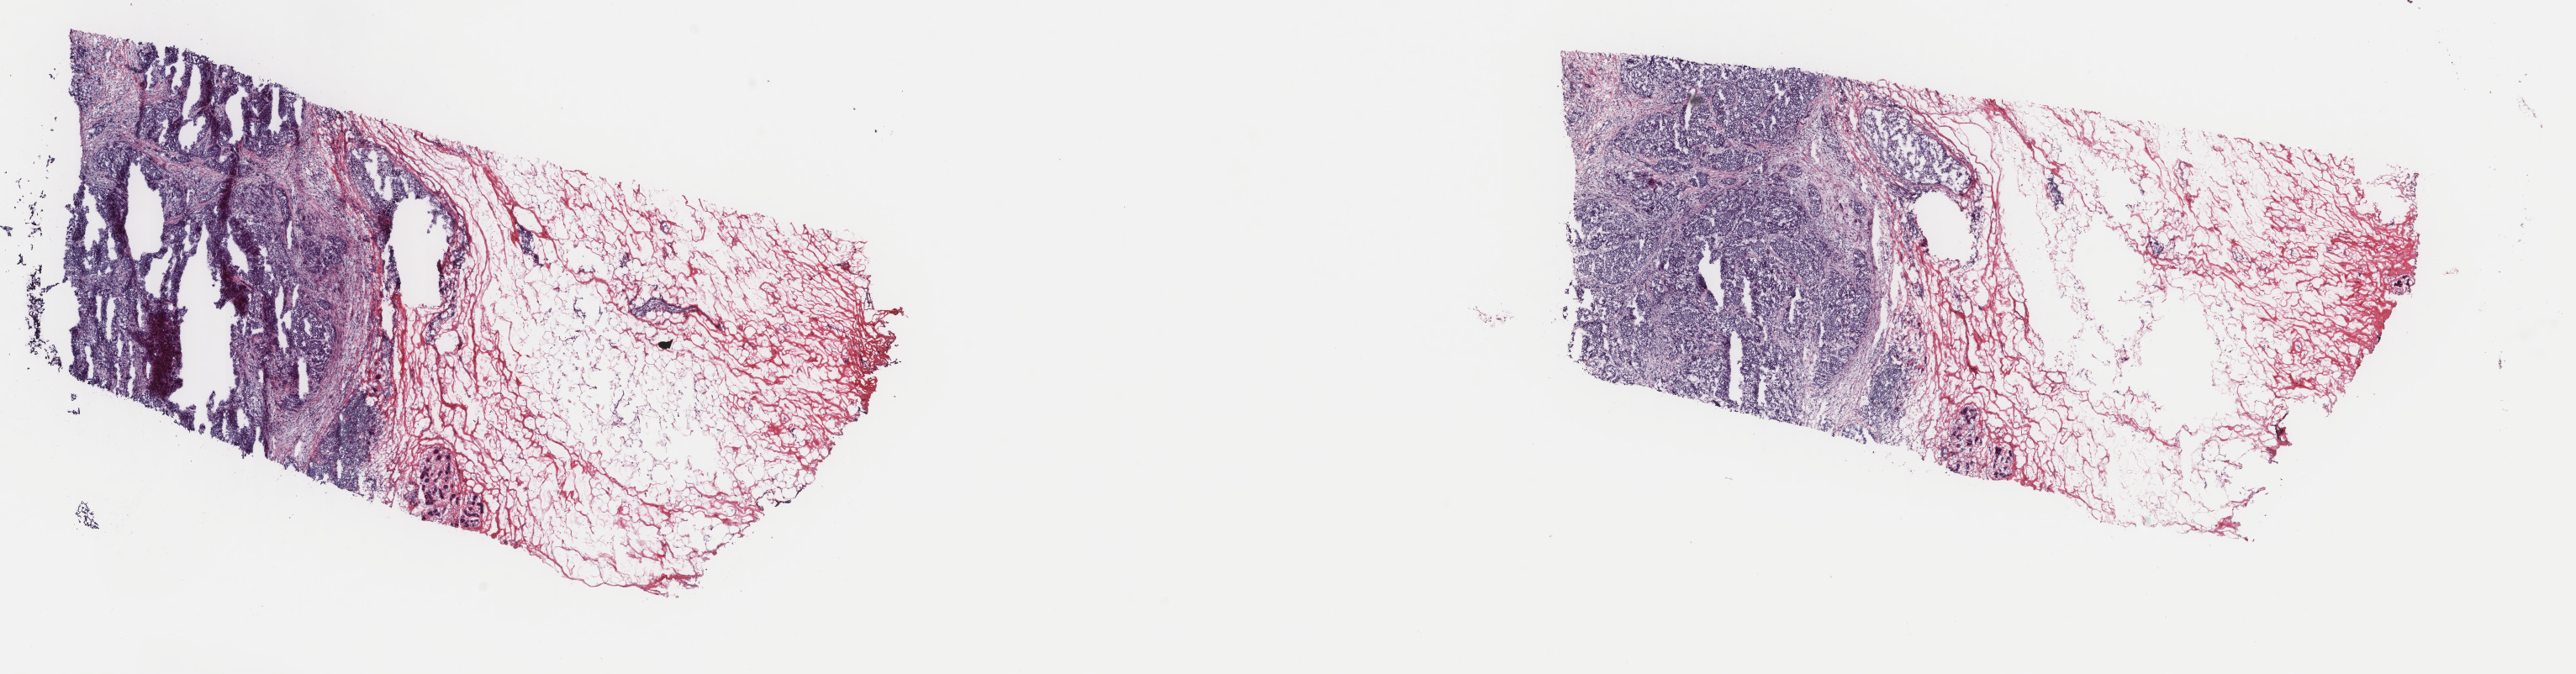
Digitized H&E-stained tissue section (whole slide) — a low-resolution overview of the entire scanned area, about 24.3 x 6.4 mm (slide scanned at 40x). Frozen section from the top of the tissue portion. Primary tumour sample from the breast. Female, age 46 years at initial diagnosis. Pathologist review of this section (percent, as recorded): tumour cells 40%, tumour nuclei 85%, normal cells 5%, stromal cells 52%, necrosis 3%. Inflammatory infiltration, as recorded: lymphocyte infiltration 6%, monocyte infiltration 0%, neutrophil infiltration 0%.
* AJCC pathologic stage: I
* TNM: T1c N0 M0
* histologic diagnosis: Infiltrating duct carcinoma, NOS
* lymph nodes positive (case pathology): 0 of 3 examined